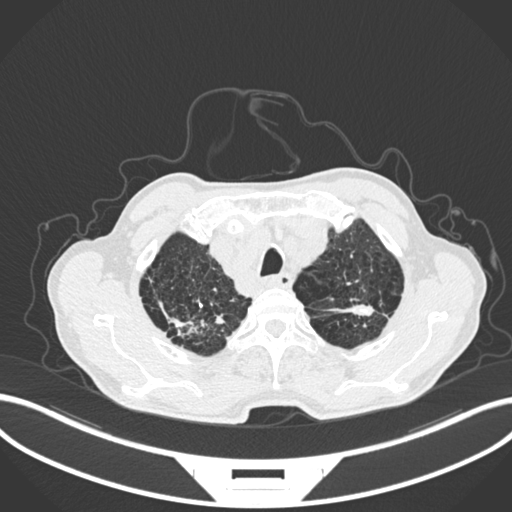
Chest CT, one axial slice. Slice 240 of 287 in the series (ordered by position). 120 kVp. Lung window (W 1500 / L -600 HU). 1 mm slice thickness. 512 × 512 image matrix. Male patient, age 74 years. From the clinical record (not read from this slice): clinical TNM (as recorded): T2a N1 M0.
Outlined on this slice (rectangle marked by the reading radiologist):
- lung tumour (recorded histology: adenocarcinoma): box from (x=326, y=301) to (x=378, y=321) px